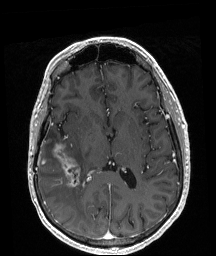
Brain MRI from a brain-tumour surgery series, one axial slice; slice 99 of 208 in the series (ordered by position); T1-weighted post-contrast; 1 mm slice thickness; 216 × 256 image matrix, field of view 211 × 250 mm. From the clinical record (not read from this slice): histopathology: Astrocytoma; WHO grade: 4; IDH mutation: yes; tumour location: Right Temporal.
Structures marked on this image (expert manual segmentation):
- tumour: bounding box (x1, y1, x2, y2) in pixels: (42, 144, 80, 187)